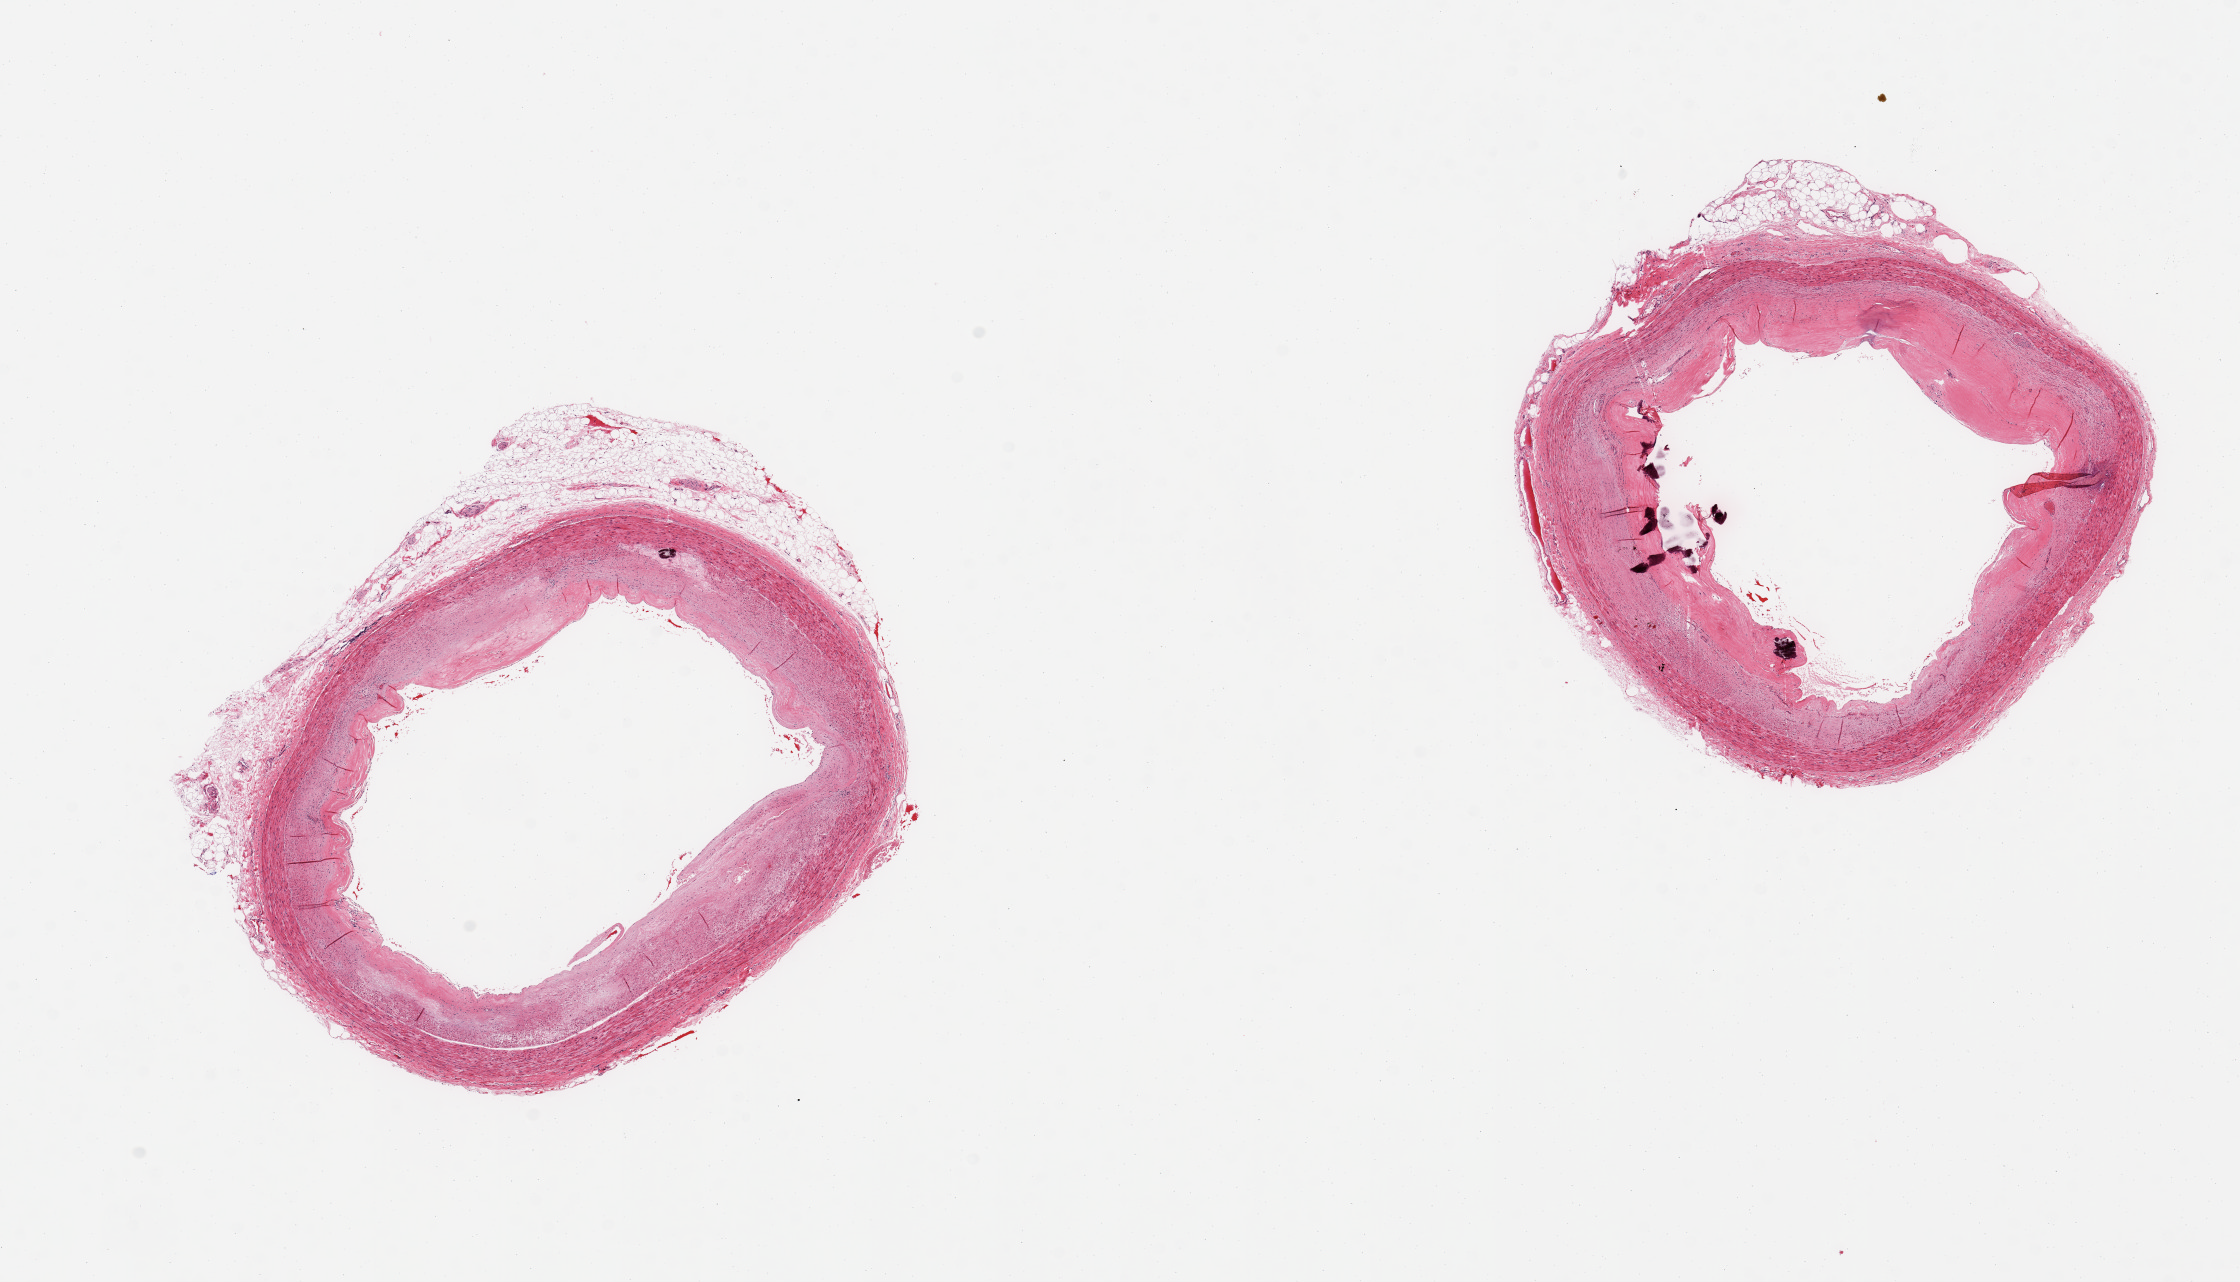
Digitized hematoxylin and eosin (H&E)-stained section, whole scanned area (about 17.7 x 10.1 mm, acquisition: 20x scan) shown as a low-resolution overview, PAXgene-fixed, paraffin-embedded tissue, sampled site (target tissue): coronary artery, donor tissue sample. Donor sex: male.
- review note (as recorded): 2 pieces; calcific atherosclerosis with mild narrowing of the lumen, minimal attached fat